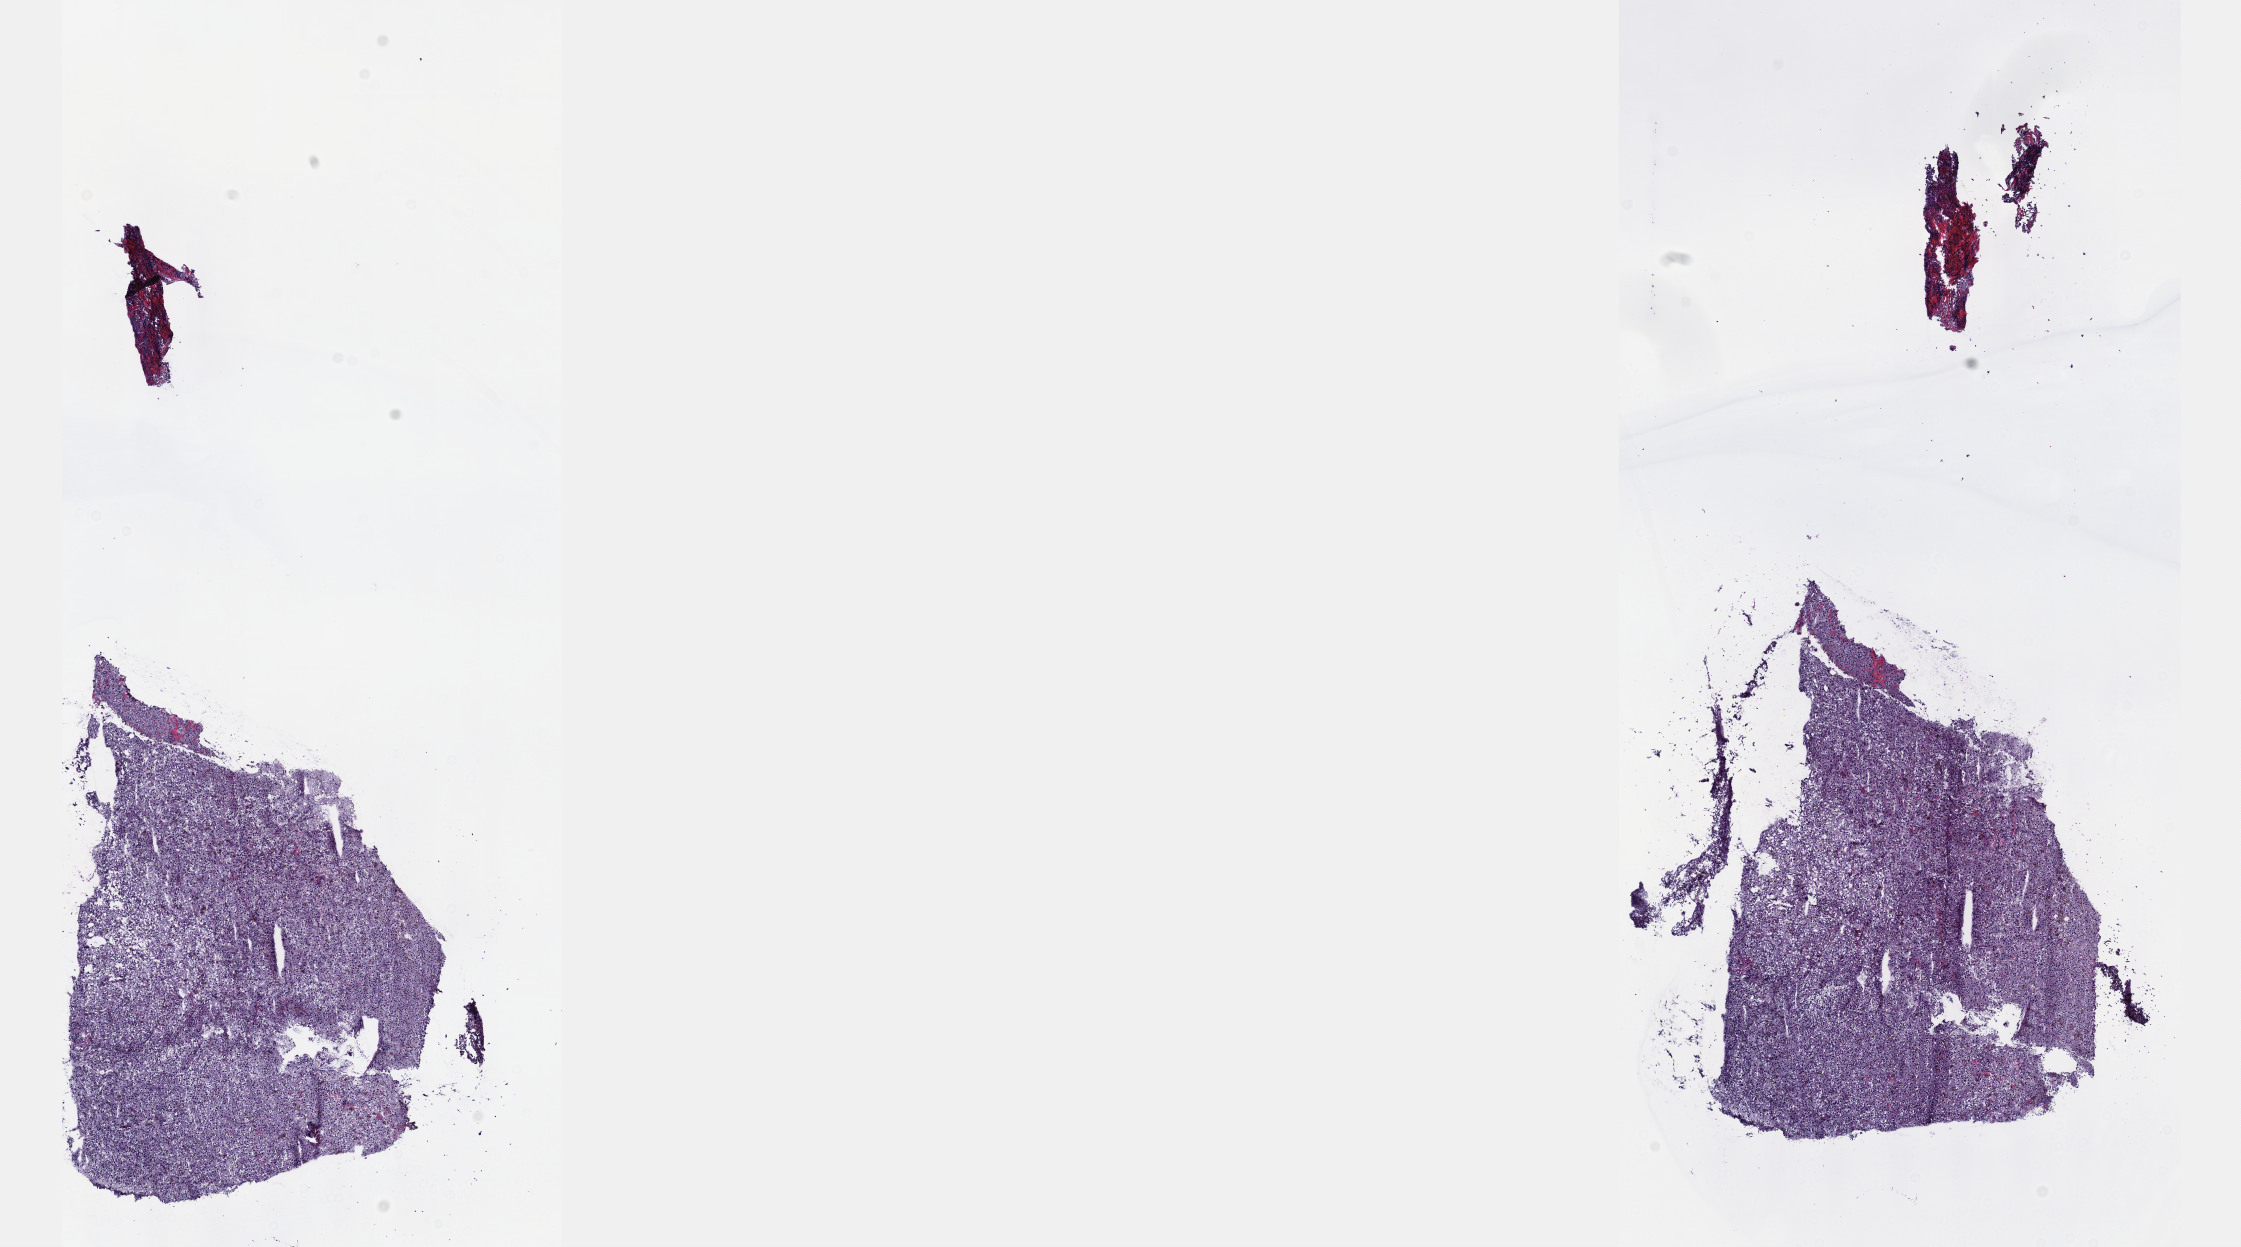
H&E-stained whole-slide image — a low-resolution overview of the entire scanned area, about 18.1 x 10.1 mm (from a 40x scan), frozen section, primary tumour sample from the skin. Male patient; age at initial diagnosis 73 years. Composition of this section per pathologist review: tumour cells 100%, tumour nuclei 80%, normal cells 0%, stromal cells 0%, necrosis 0%. Inflammatory infiltration, as recorded: lymphocyte infiltration 3%, monocyte infiltration 0%, neutrophil infiltration 0%.
Histologic diagnosis: Malignant melanoma, NOS.